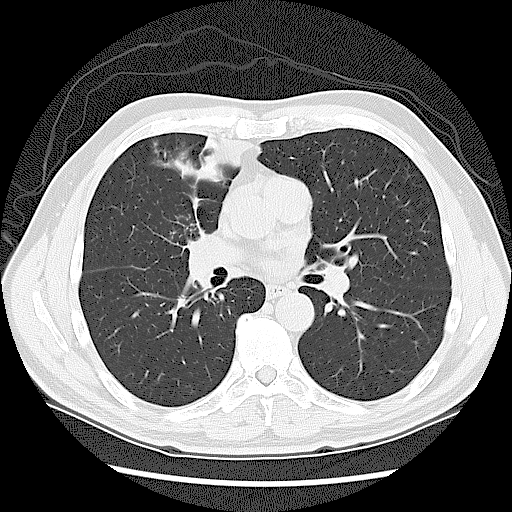
Low-dose screening chest CT, axial slice. Baseline screening round. Lung window (W 1500 / L -600 HU). 2.5 mm slice thickness. Lung (sharp) reconstruction kernel (LUNG). Slice 64 of 131 in the series. 512 × 512 image matrix. Male participant, aged 60 years at enrolment. Current smoker at enrolment.
Lesion marked by an expert reader, box from (x=158, y=214) to (x=240, y=303) px. Screening reader's record for this exam: no non-calcified nodule ≥4 mm recorded. Official screen result: negative screen, significant abnormalities not suspicious for lung cancer. Participant outcome: lung cancer diagnosed 41 days after this screen — small cell carcinoma, NOS, right upper lobe, stage IIIA (AJCC 6th edition).